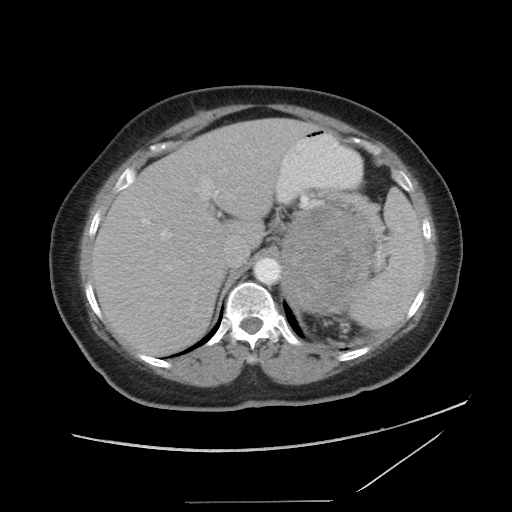
Contrast-enhanced abdominal CT, one axial slice; slice 64 of 86 in the series (ordered by position); reconstruction kernel STANDARD; intravenous contrast given; soft-tissue window (W 400 / L 40 HU); 5 mm slice thickness; 512 × 512 image matrix, field of view 398 × 398 mm. Patient: female, 77 years. Case-level facts recorded for this patient, not image findings: diagnosis: adrenocortical carcinoma; tumour side: left adrenal; tumour size at pathology: 13.1 cm; Ki-67 index: 10 %; stage (as recorded): 3.
Structures marked on this image (semi-automatic segmentation, software-assisted and operator-edited):
- mass: bounding box <283,204,370,312> (left, top, right, bottom; pixels)